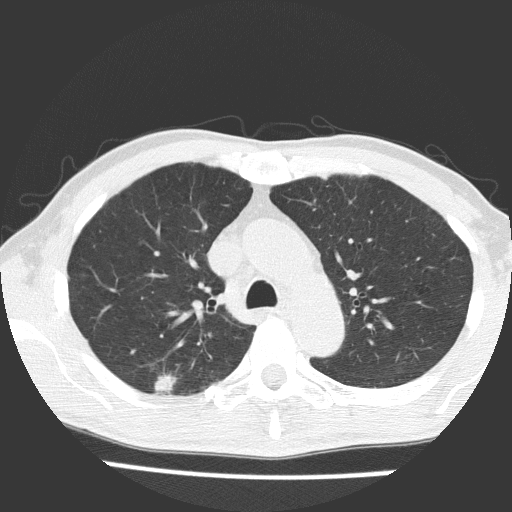
Low-dose screening chest CT, one axial slice; slice 114 of 160 in the series (ordered by position); reconstruction kernel FC51; 120 kVp; lung window (W 1500 / L -600 HU); 512 × 512 image matrix, field of view 309 × 309 mm.
Annotated regions visible in this slice (manually delineated by an expert):
- lesion 1 (tumor, upper lobe of right lung): box from (x=154, y=373) to (x=178, y=393) px